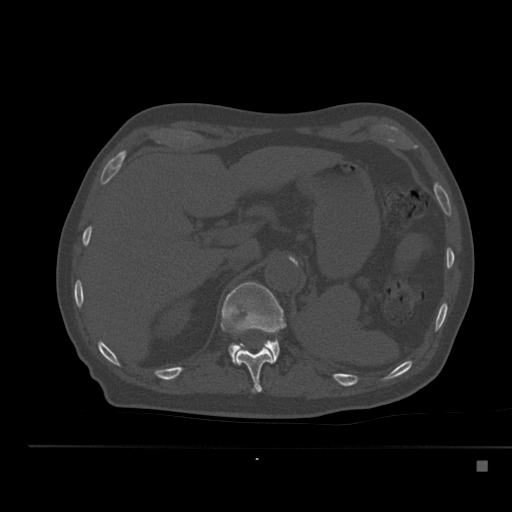
CT including the spine, one axial slice. Slice 241 of 517 in the series (ordered by position). Reconstruction kernel Br40s. 120 kVp. Bone window (W 1800 / L 400 HU). 512 × 512 image matrix, field of view 408 × 408 mm. Patient: male, 70 years. Case-level facts recorded for this patient, not image findings: primary cancer: renal; vertebrae with lytic lesions (as recorded): T4, T6, T10, T12, L3, L4, L5.
Structures marked on this image (semi-automatically segmented with operator editing):
- T11 vertebra: bounding box [x1, y1, x2, y2] px = [236, 332, 273, 393]
- T12 vertebra: [221, 282, 286, 365]